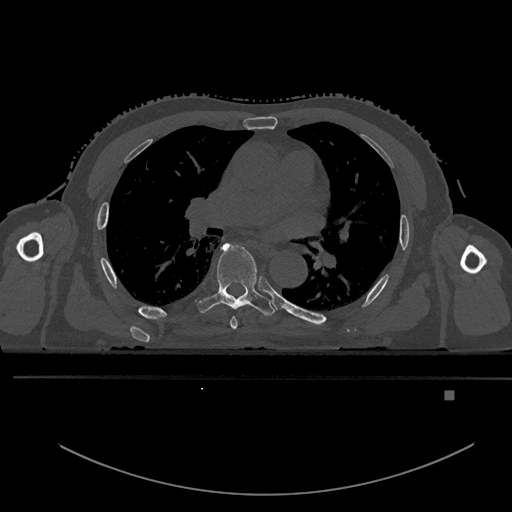
CT including the spine, one axial slice. Position 316 of 969 along the scan axis. Bone window (W 1800 / L 400 HU). 512 × 512 image matrix, field of view 456 × 456 mm. Patient: male, 82 years. From the clinical record (not read from this slice): primary cancer: prostate; vertebrae with lytic lesions (as recorded): T11, T9, T8, T2.
Outlined on this slice (semi-automatic segmentation, software-assisted and operator-edited):
- T5 vertebra: box from (x=230, y=317) to (x=238, y=330) px
- T6 vertebra: (x=196, y=243)–(x=276, y=316)